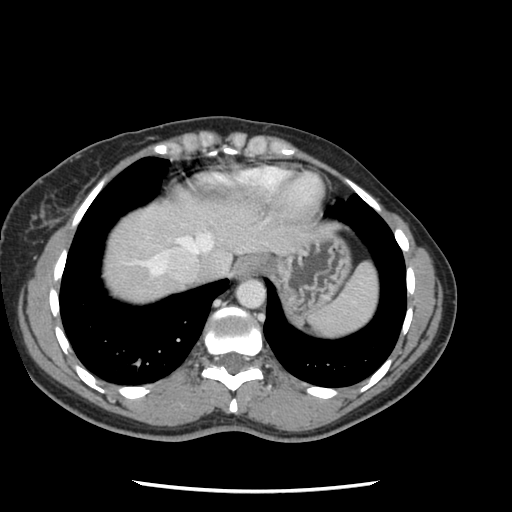
Contrast-enhanced abdominal CT, one axial slice. Position 109 of 134 along the scan axis. 120 kVp. Soft-tissue window (W 400 / L 40 HU). 2.5 mm slice thickness. 512 × 512 image matrix. Female patient, age 43 years. Case-level facts recorded for this patient, not image findings: diagnosis: colorectal cancer liver metastases, imaged before liver resection; multiple liver metastases: yes; largest metastasis: 3.4 cm.
Structures marked on this image (outlined manually by an expert reader):
- hepatic veins: bounding box <142,233,213,276> (left, top, right, bottom; pixels)
- liver: <102,201,270,303>
- planned liver remnant (the part of the liver to remain after resection): <102,201,201,292>